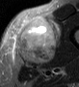
MRI of an extremity soft-tissue mass, one axial slice; position 24 of 45 along the scan axis; STIR; MR volume resampled by the dataset authors to the PET/CT grid (not the native acquisition matrix); 3.27 mm slice thickness; 79 × 87 image matrix, field of view 77 × 85 mm. Male patient. From the clinical record (not read from this slice): histological type: pleiomorphic leiomyosarcoma; grade: high; site of the primary tumour: left thigh.
Outlined on this slice (expert contour drawn on MRI and transferred to this co-registered scan by the dataset authors):
- gross tumour volume including surrounding oedema: bounding box [x1, y1, x2, y2] px = [15, 16, 60, 65]
- gross tumour volume (mass): [15, 16, 57, 65]